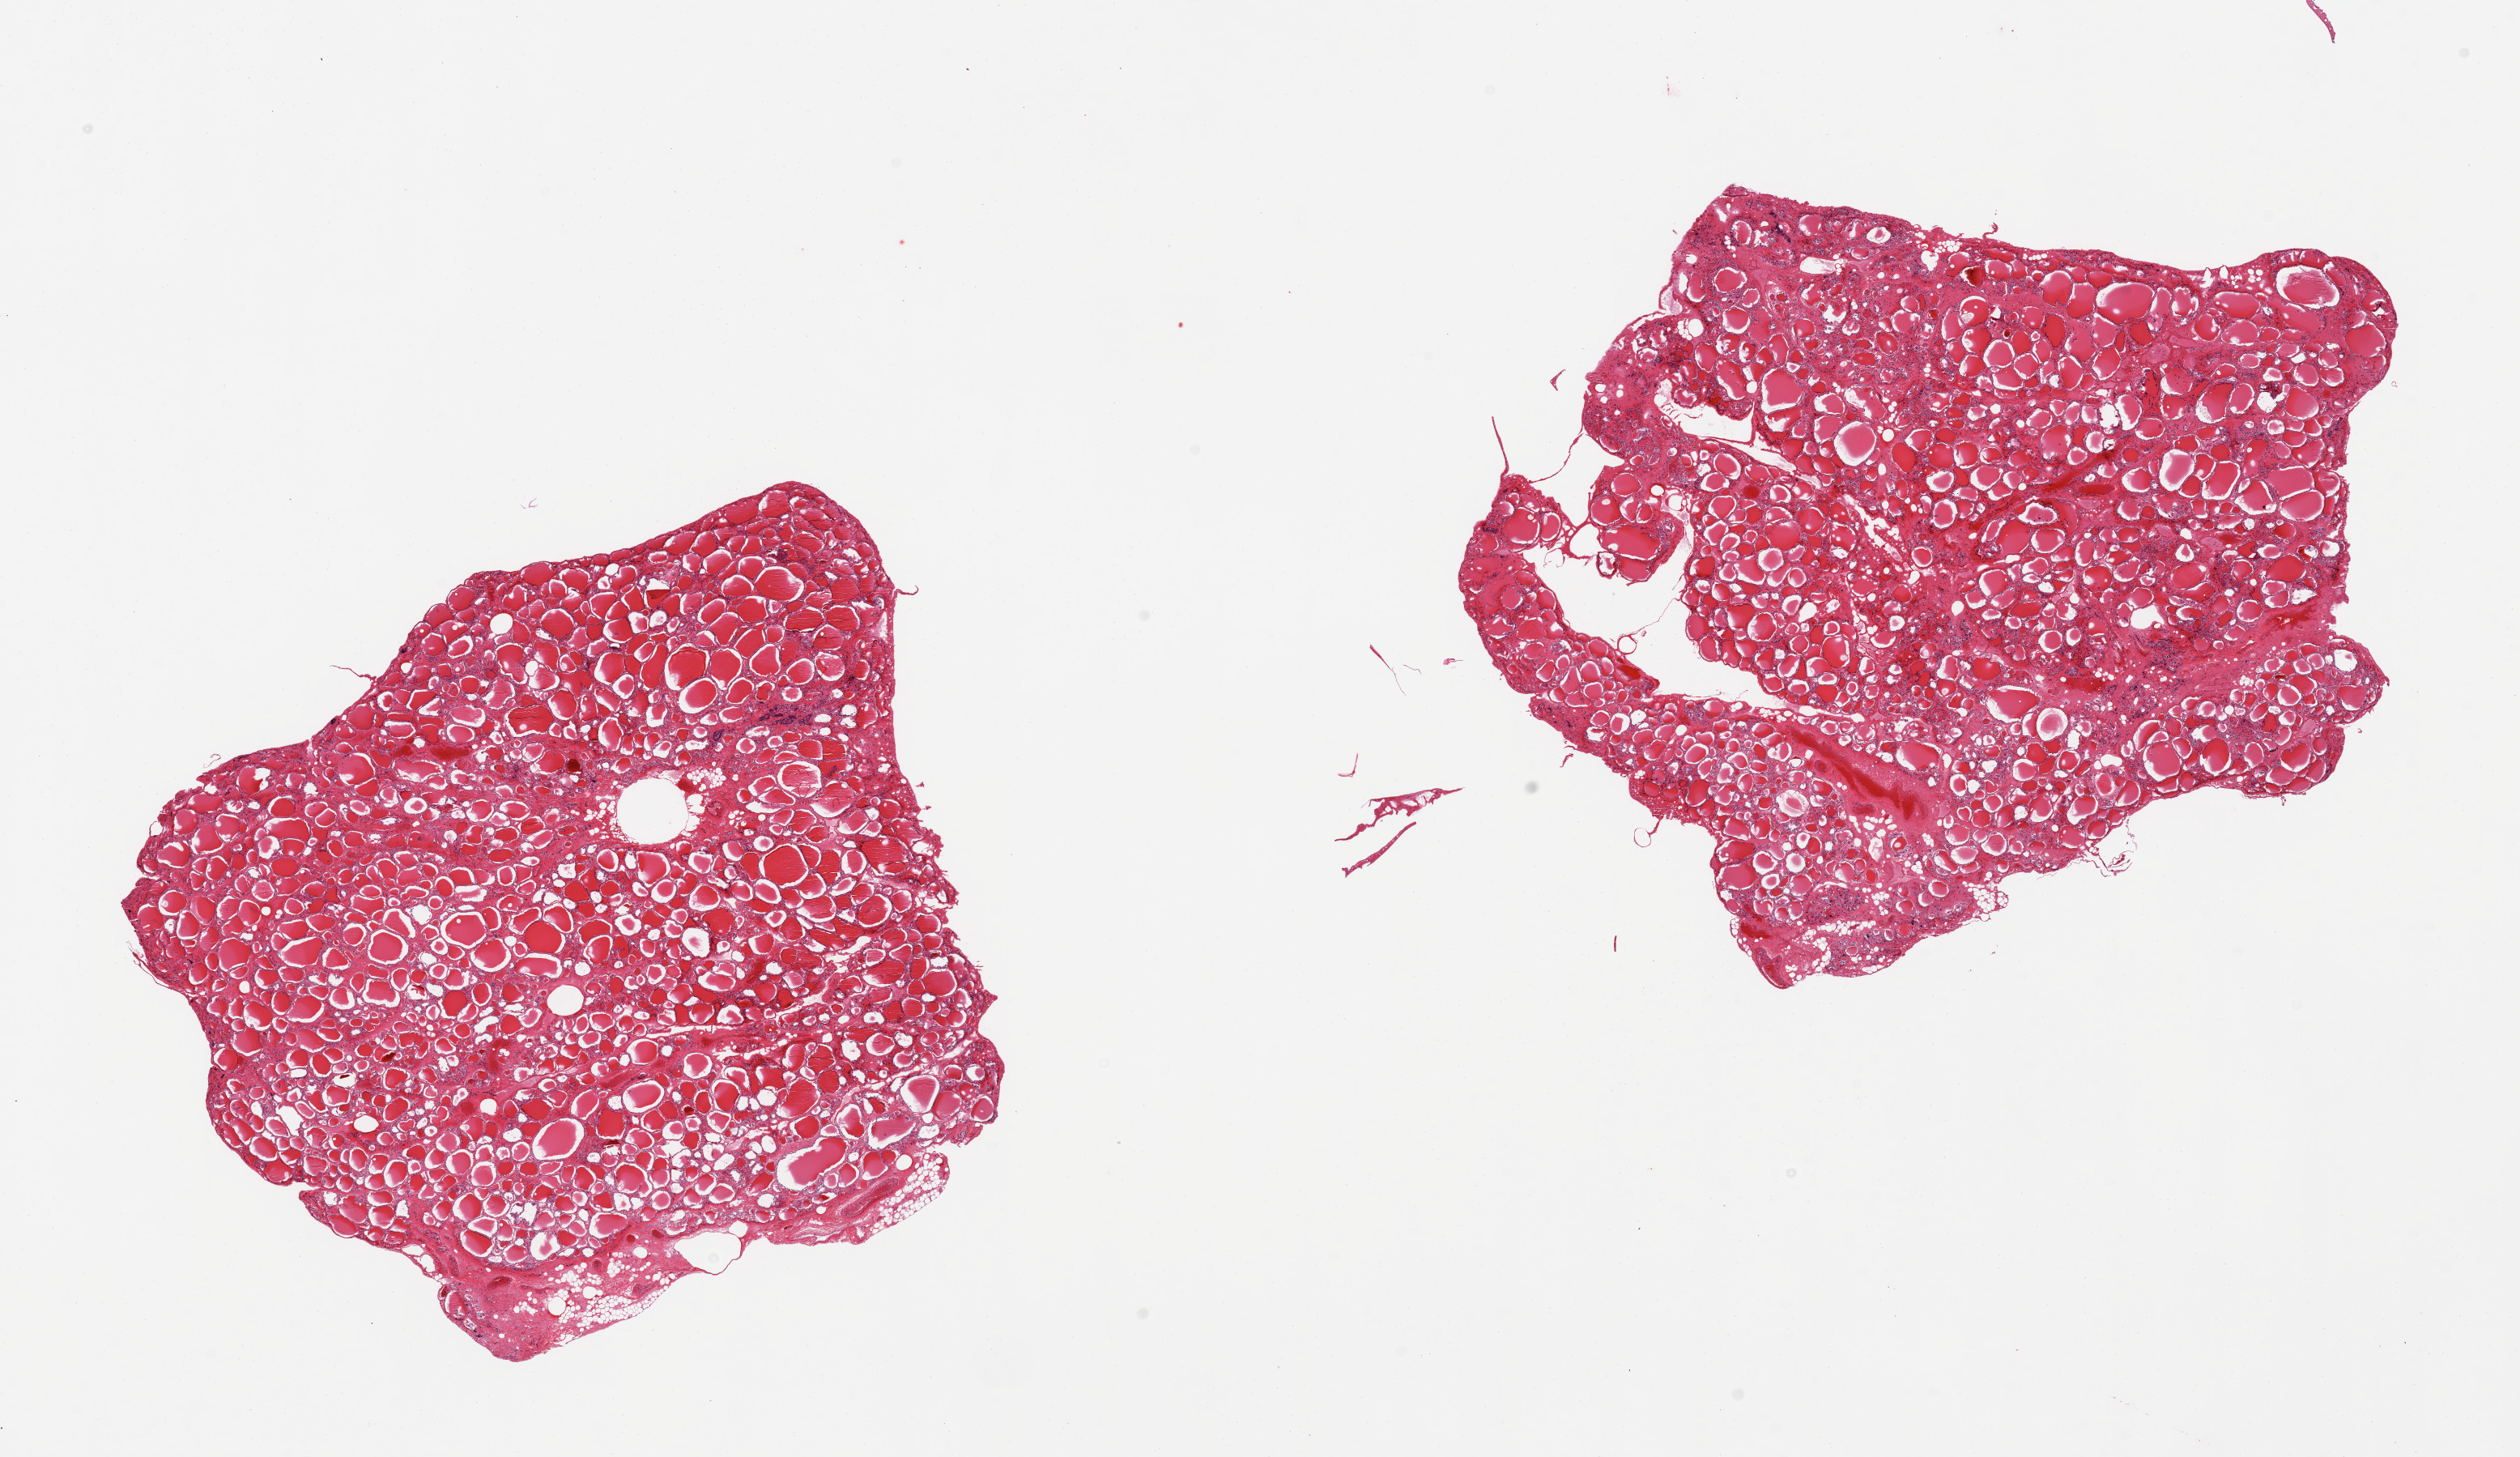
Hematoxylin and eosin (H&E) whole-slide image — low-resolution overview of the scanned area, about 24.6 x 14.2 mm (acquisition: 20x scan); PAXgene-fixed, paraffin-embedded tissue; sampled site (target tissue): thyroid; donor tissue sample.
Reviewer comment on this tissue sample: 2 pieces.